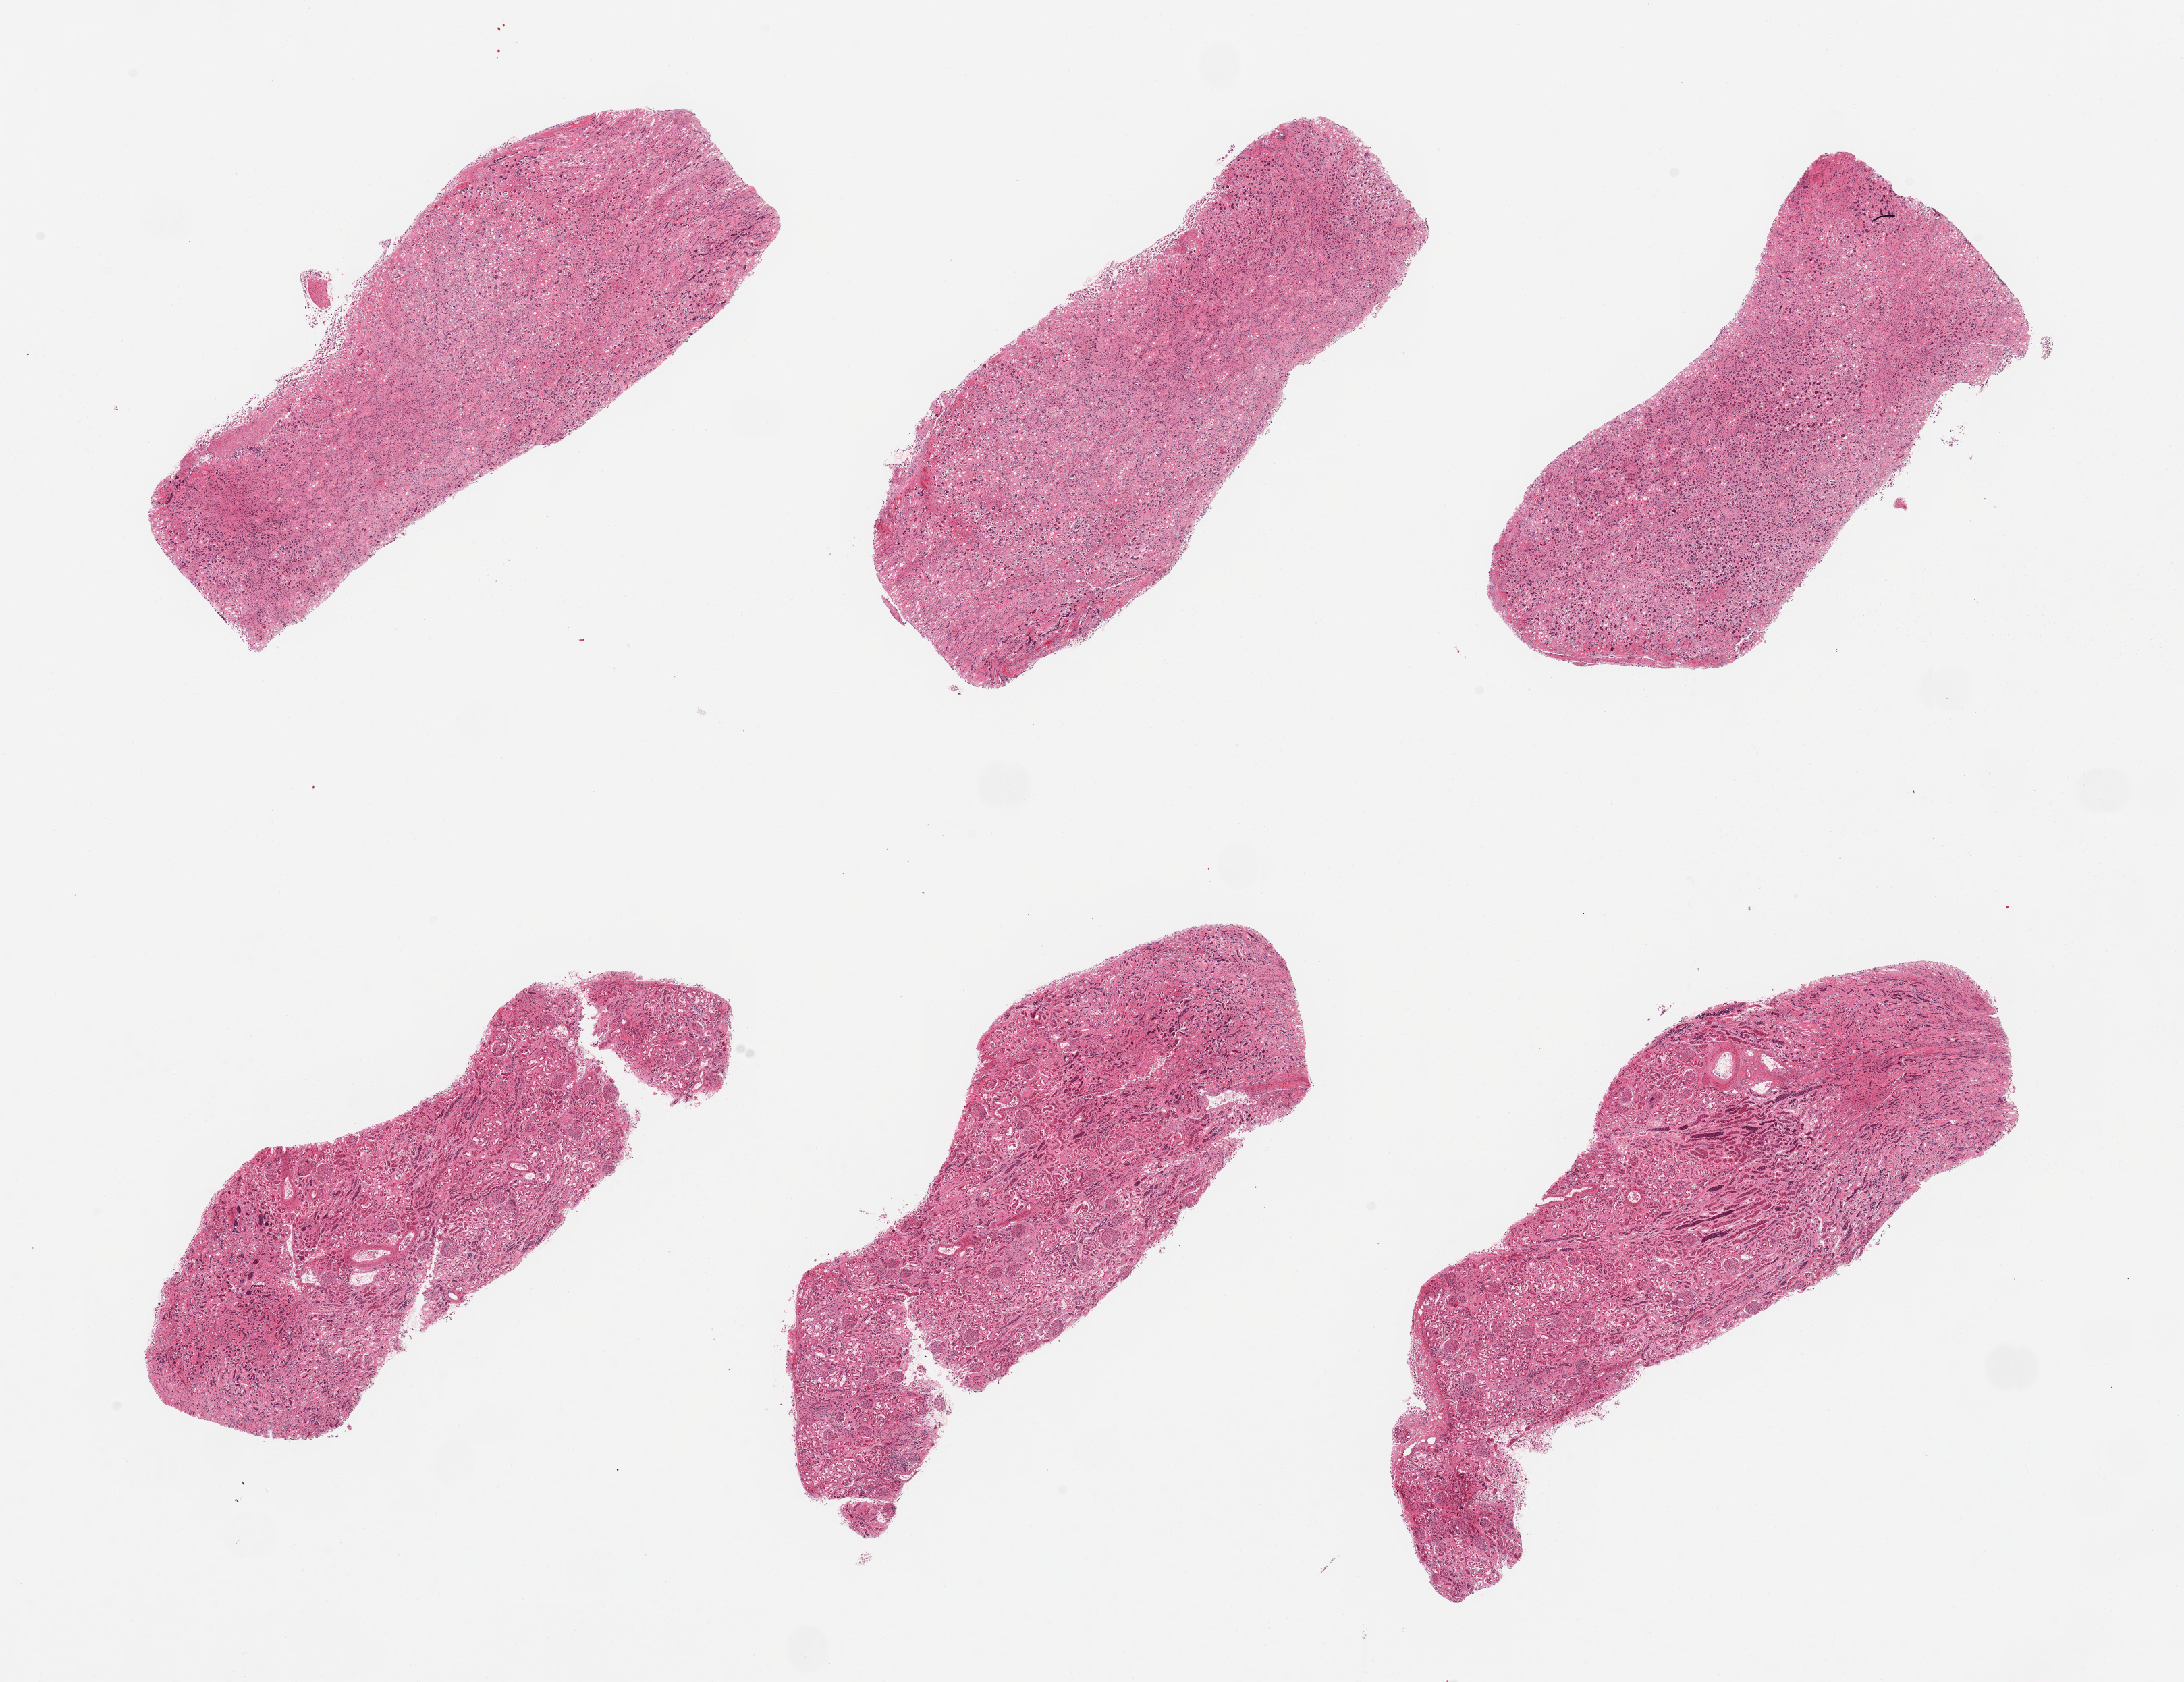
Digitized hematoxylin and eosin (H&E)-stained section — low-resolution overview of the scanned area, about 25.6 x 19.7 mm (from a 20x scan); PAXgene-fixed paraffin-embedded (PFPE) section; sampled site (target tissue): renal cortex; tissue donor sample. Donor: female.
• review note (as recorded): 6 pieces, cortex and medulla